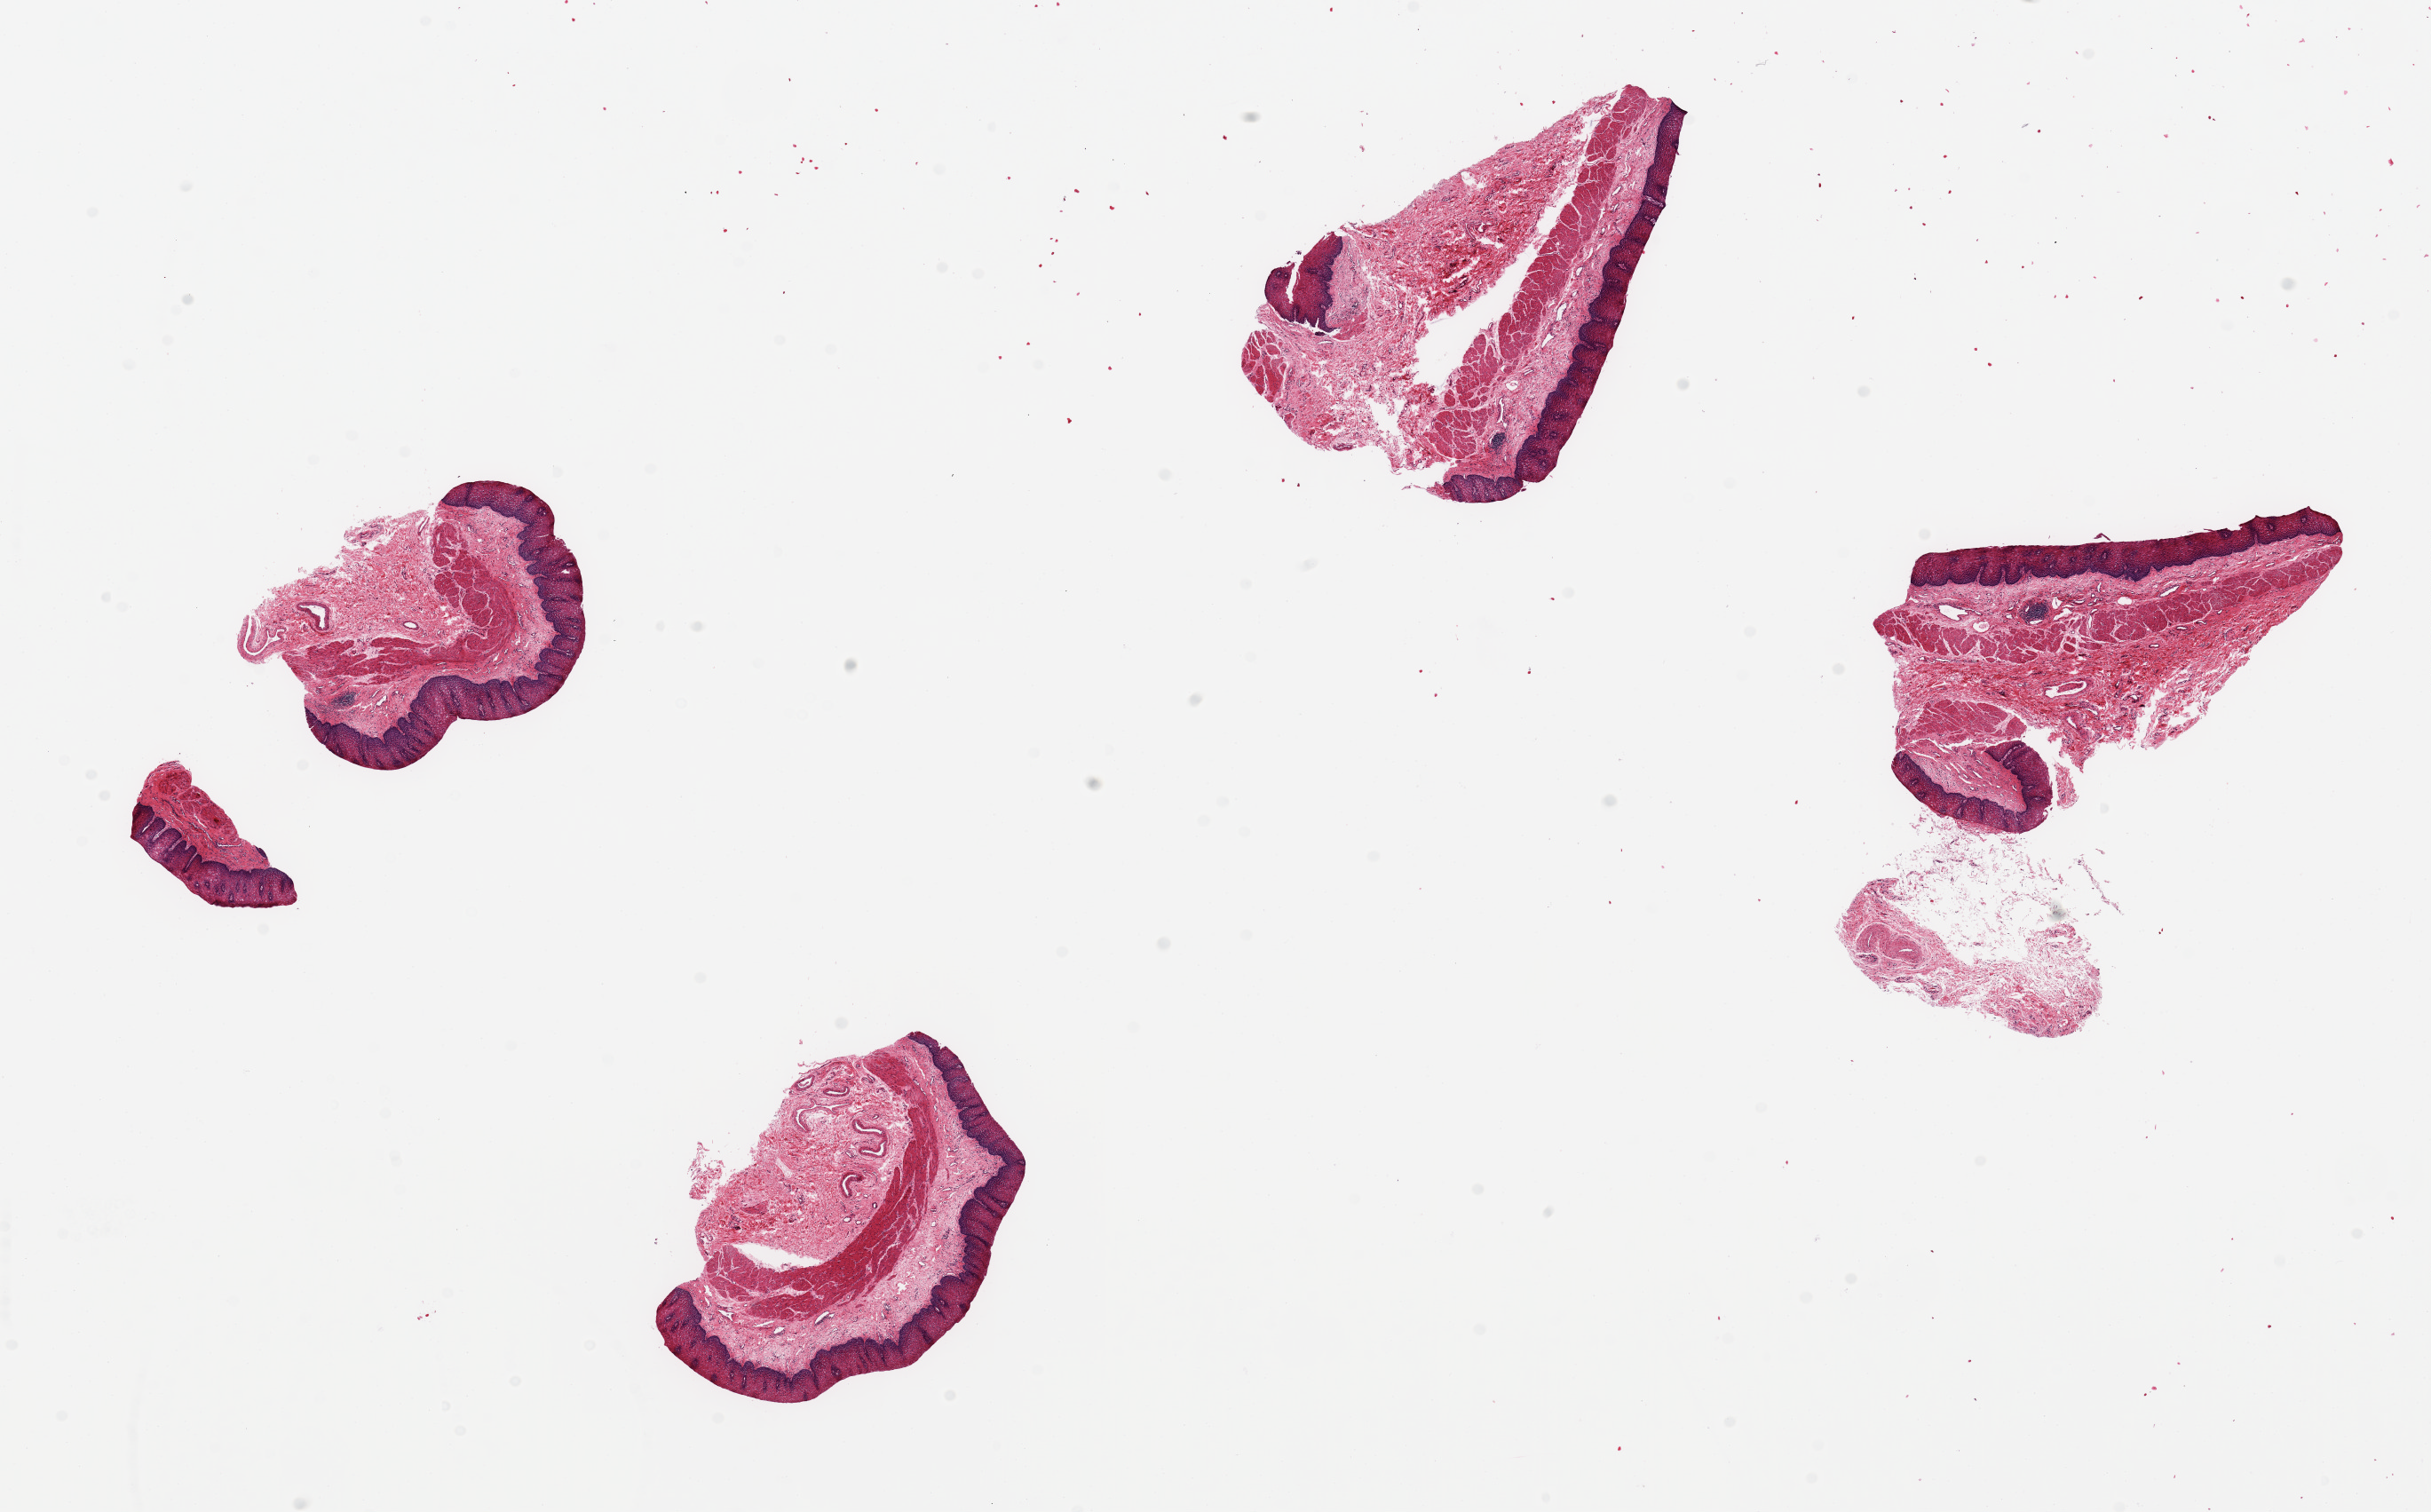
Hematoxylin and eosin (H&E) whole-slide image — whole scanned area (about 21.7 x 13.5 mm, acquisition: 20x scan) shown as a low-resolution overview; PAXgene-fixed, paraffin-embedded tissue; sampled site (target tissue): esophageal mucous membrane; tissue donor sample. Male donor.
- review note (as recorded): 4 ~ 3x2.5mm pieces; mucosae is ~10 of specimen thickness